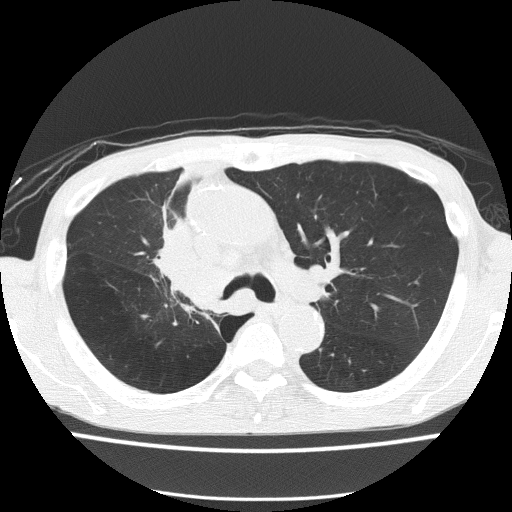
Low-dose screening chest CT, one axial slice. Slice 99 of 150 in the series (ordered by position). Reconstruction kernel FC51. 120 kVp. Lung window (W 1500 / L -600 HU). 512 × 512 image matrix, field of view 336 × 336 mm.
Outlined on this slice (outlined manually by an expert reader):
- lesion 1 (tumor, hilum of right lung): bounding box <158,220,224,311> (left, top, right, bottom; pixels)